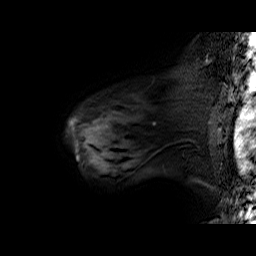
Breast MRI (dynamic contrast-enhanced), one sagittal slice; position 48 of 60 along the scan axis; dynamic contrast-enhanced series, time point 2 of 6 at this slice position (early post-contrast); 1.5 T; TE 6.4 ms, TR 32.9 ms; 4 mm slice thickness; 256 × 256 image matrix, field of view 200 × 200 mm. Female patient. From the clinical record (not read from this slice): setting: breast cancer imaged before/during neoadjuvant chemotherapy; receptor status: HER2-positive.
Annotated regions visible in this slice (semi-automatically segmented with operator editing):
- analysis volume of interest (the breast-tissue region the enhancement analysis was run in; not a lesion): bounding box (x1, y1, x2, y2) in pixels: (68, 78, 196, 160)
- tumour enhancement mask (voxels above the 100 % enhancement threshold inside the analysis volume of interest): (69, 119, 79, 160)